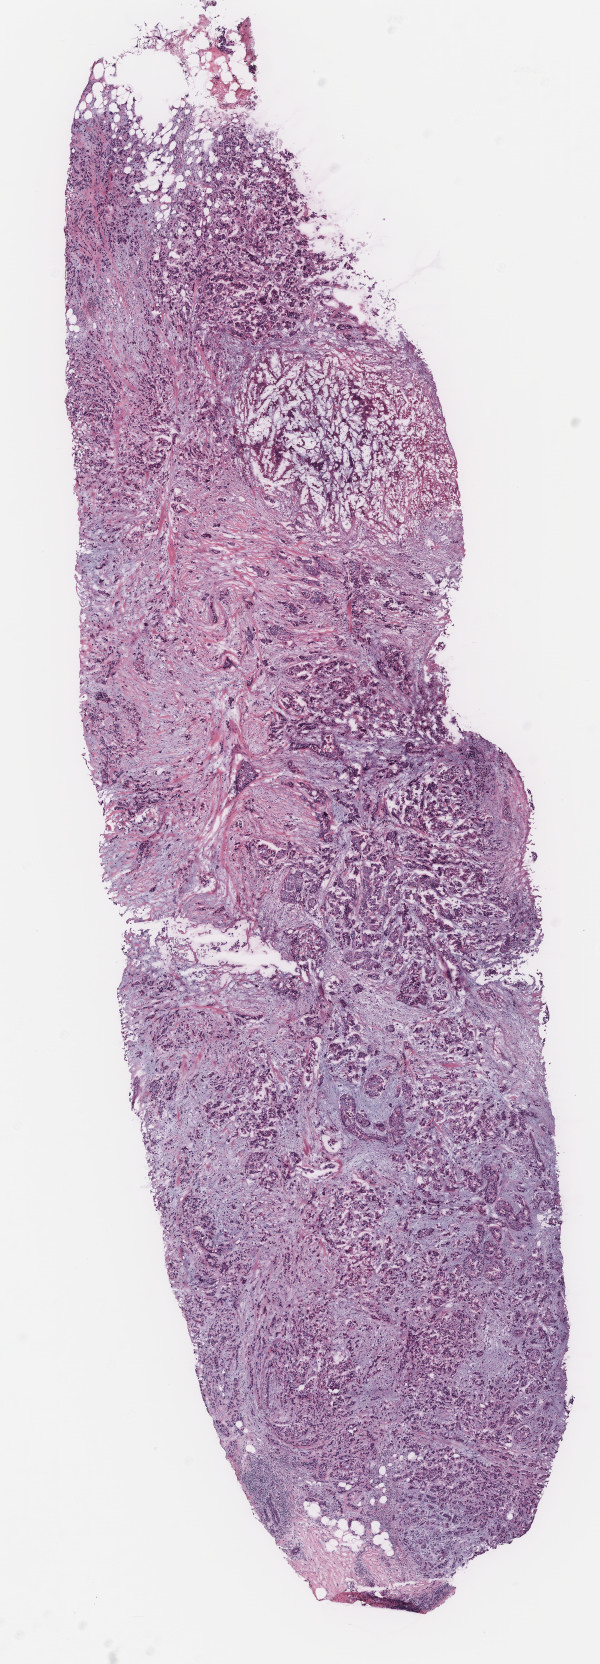
H&E-stained whole-slide image, shown as a low-resolution overview of the whole scanned area (about 4.8 x 13.3 mm), breast, tumour tissue. Female, 58 y/o.
AJCC pathologic stage: IIA. Diagnosis: Infiltrating duct carcinoma, NOS.